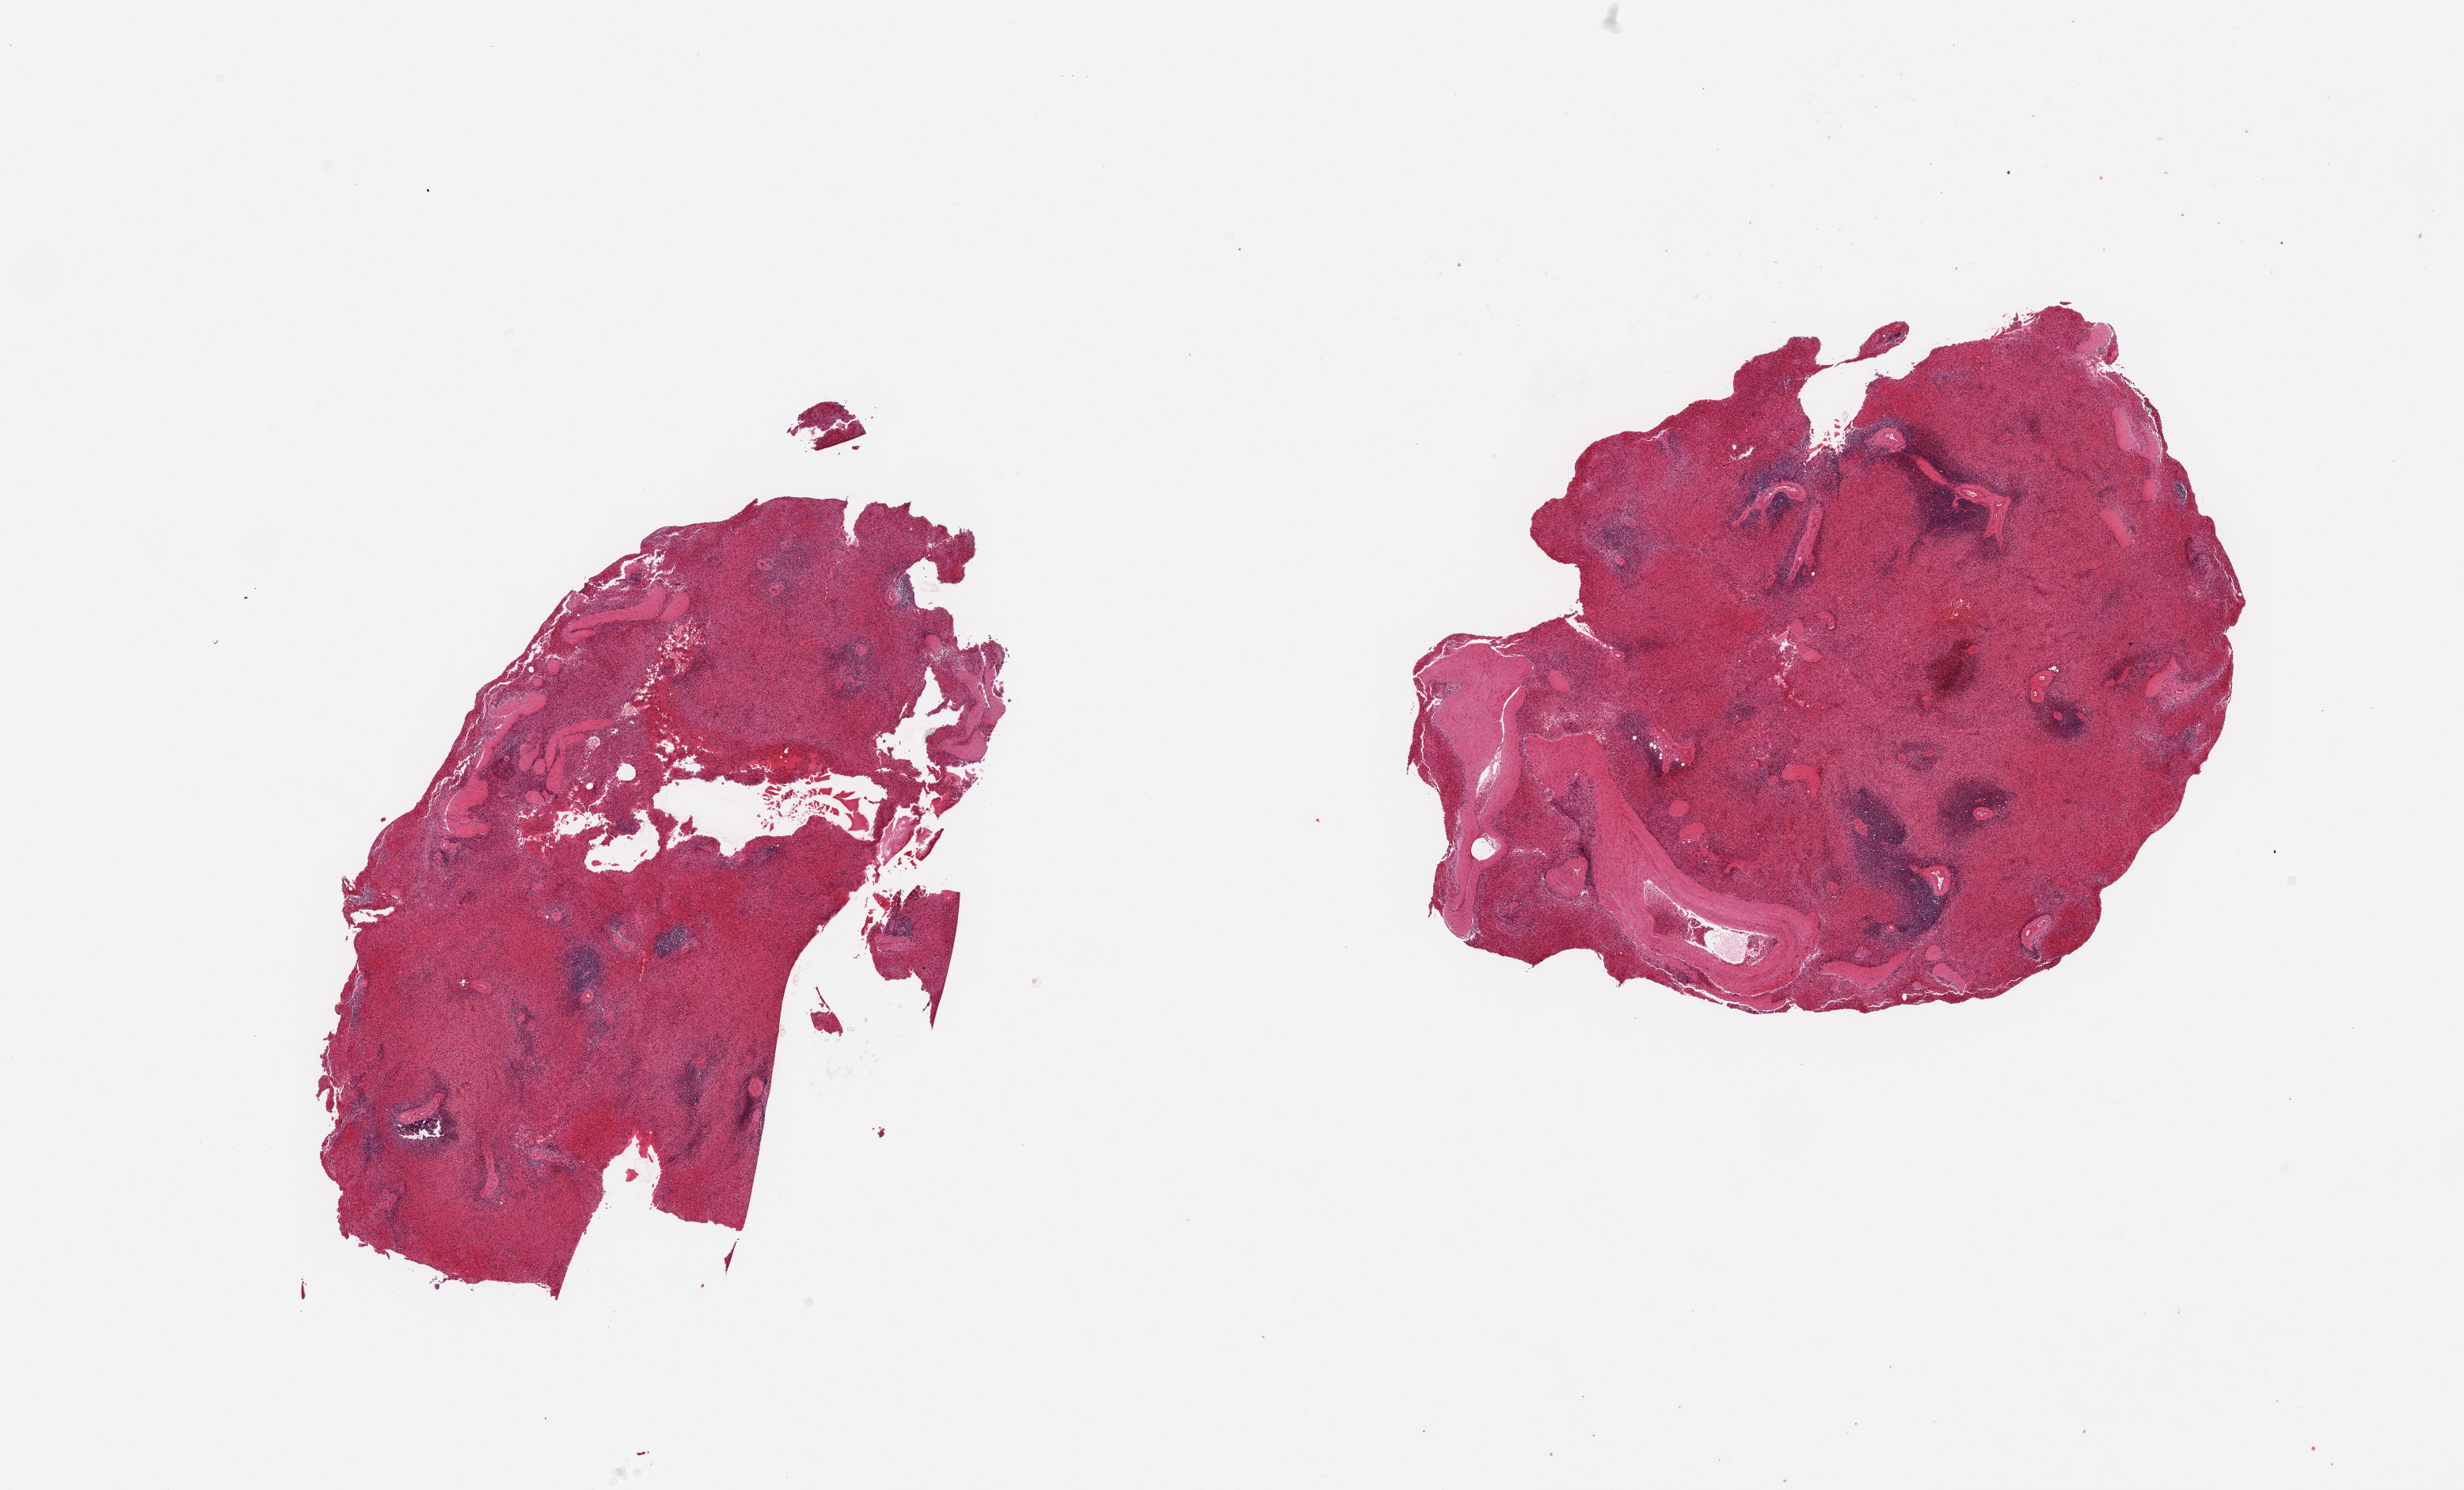
H&E whole-slide image — low-resolution overview of the scanned area, about 24.6 x 14.9 mm, PAXgene-fixed paraffin-embedded (PFPE) section, target tissue: spleen, tissue donor sample. Donor sex: male.
* reviewer comment on this tissue sample: 2 pieces; congestion